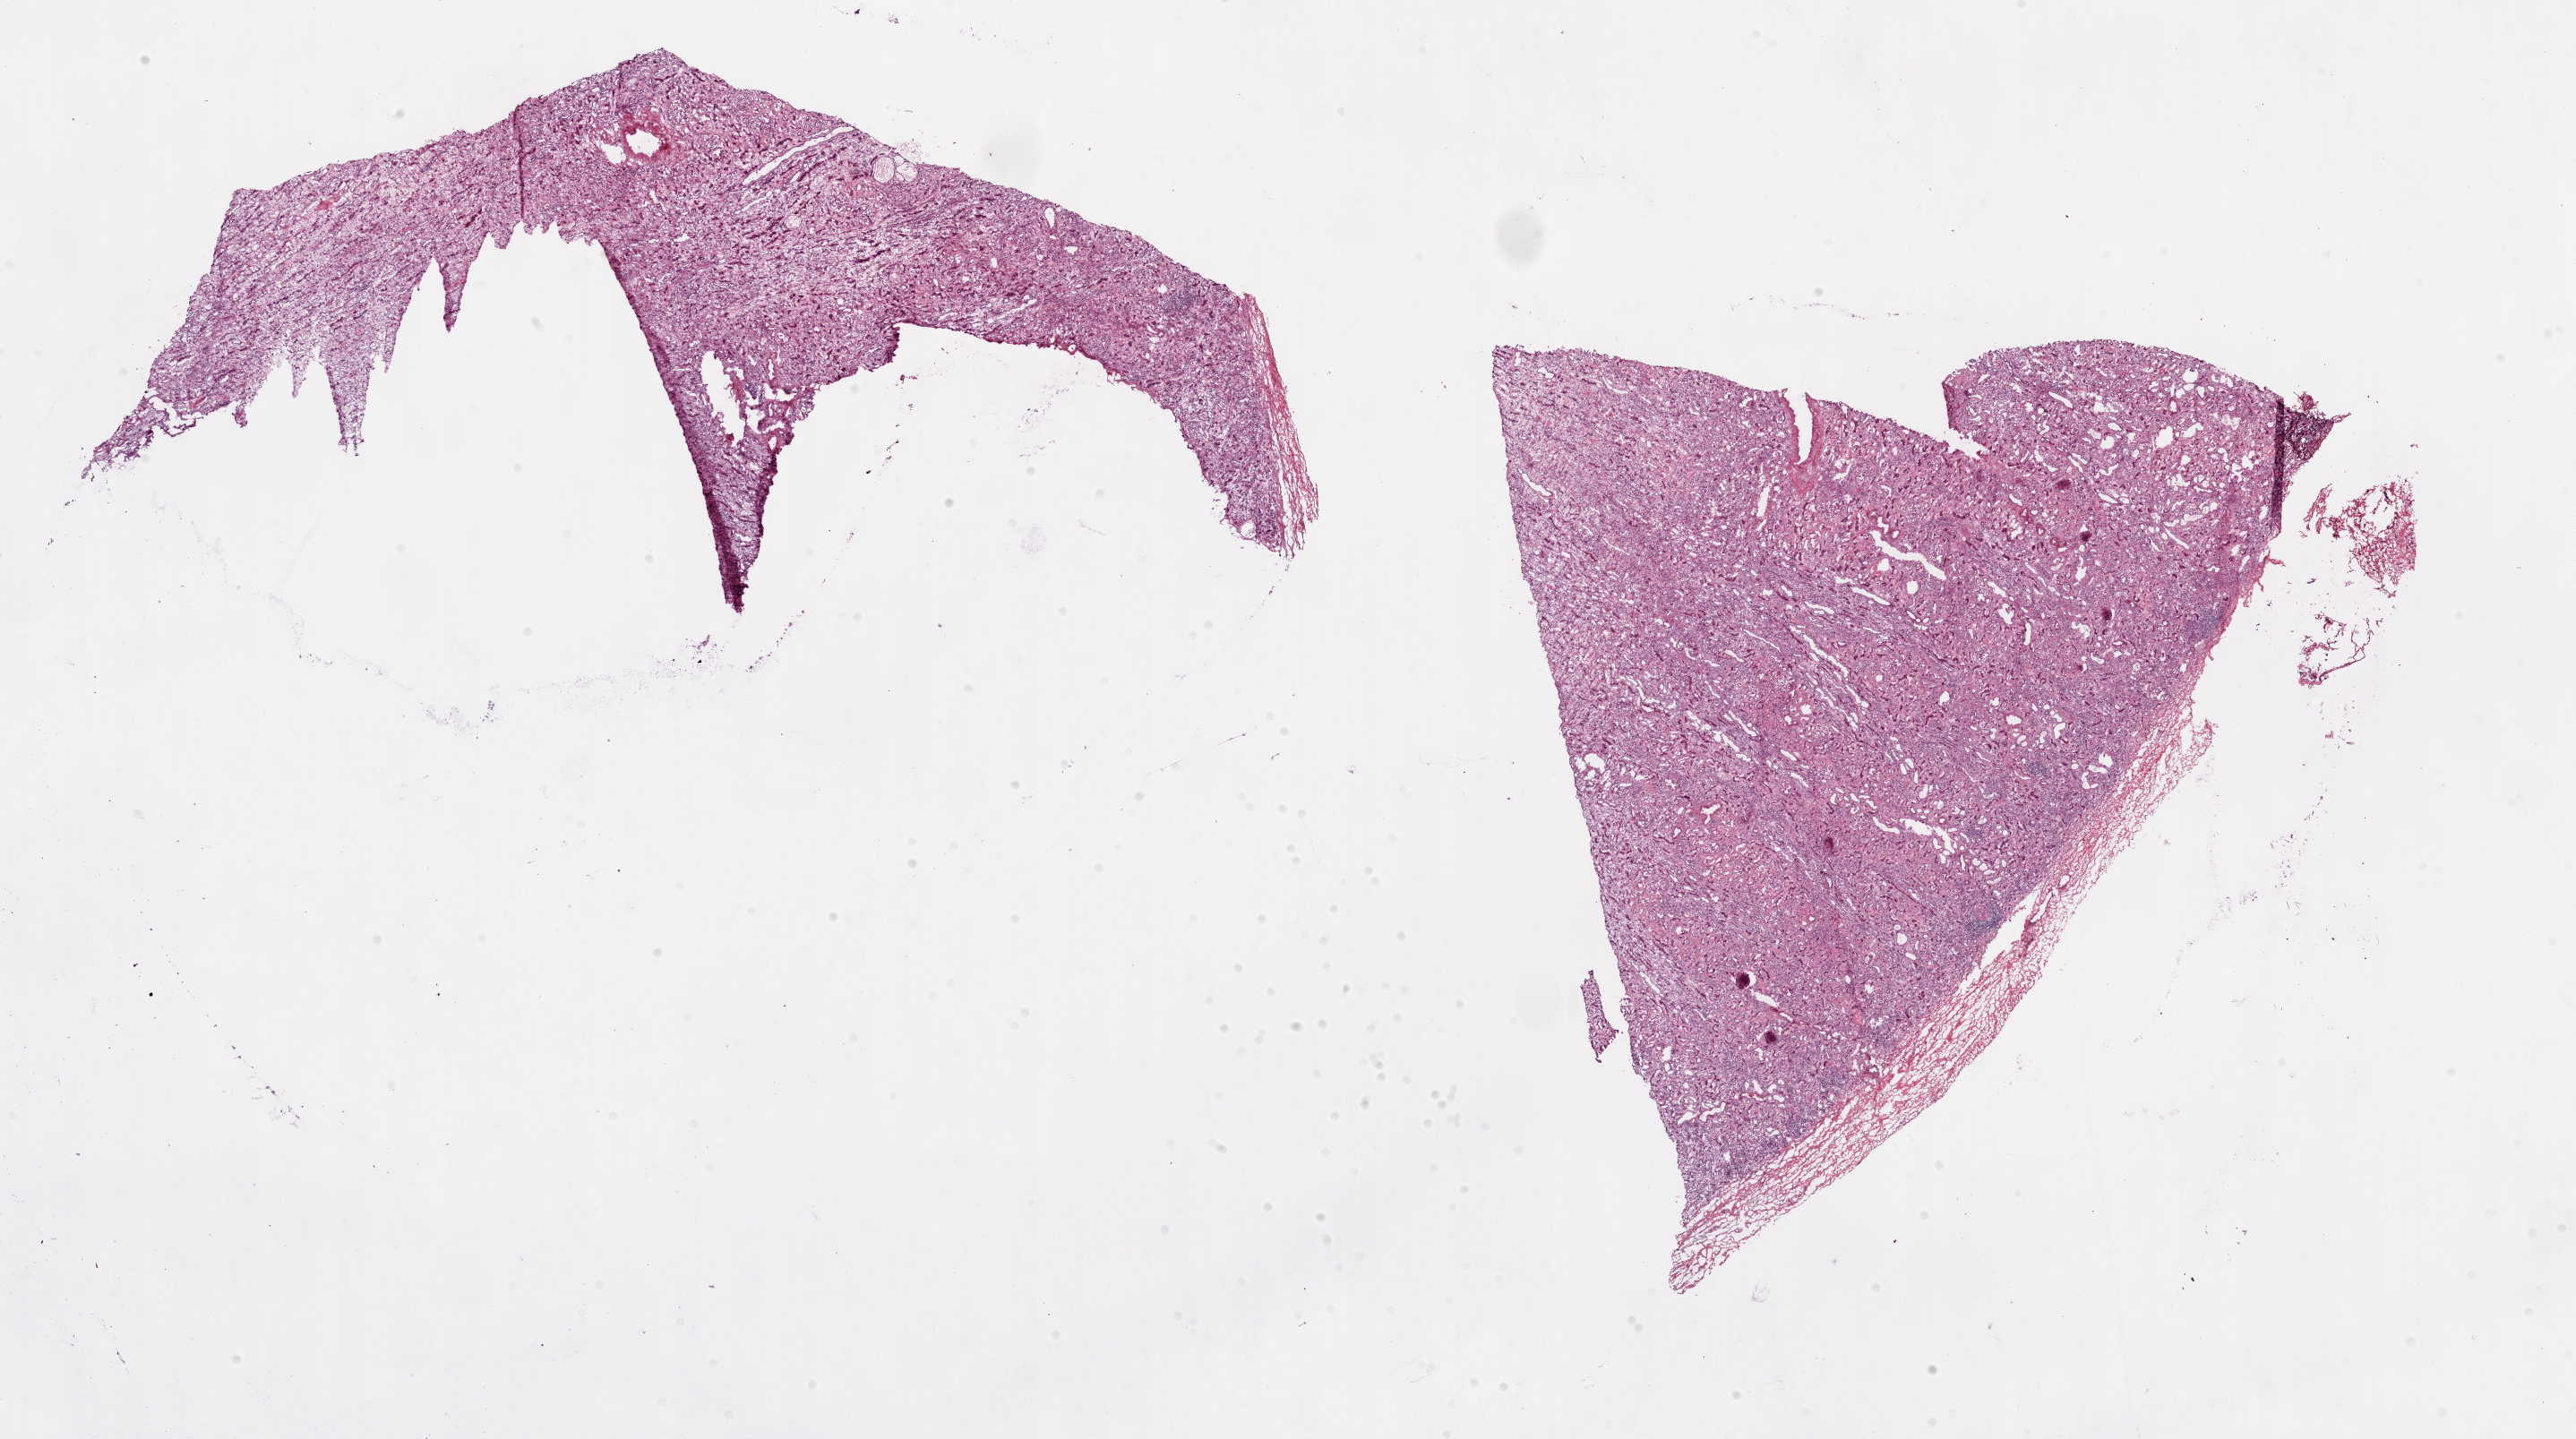
Digitized H&E tissue section (whole slide), a low-resolution overview of the entire scanned area, about 22.8 x 12.7 mm (slide scanned at 20x), frozen section from the bottom of the tissue portion, kidney, solid tissue normal (non-tumour tissue) sample. Male, age 65 years at initial diagnosis.
• this section: solid tissue normal (non-tumour) sample from the same patient
• patient diagnosis: Clear cell adenocarcinoma, NOS